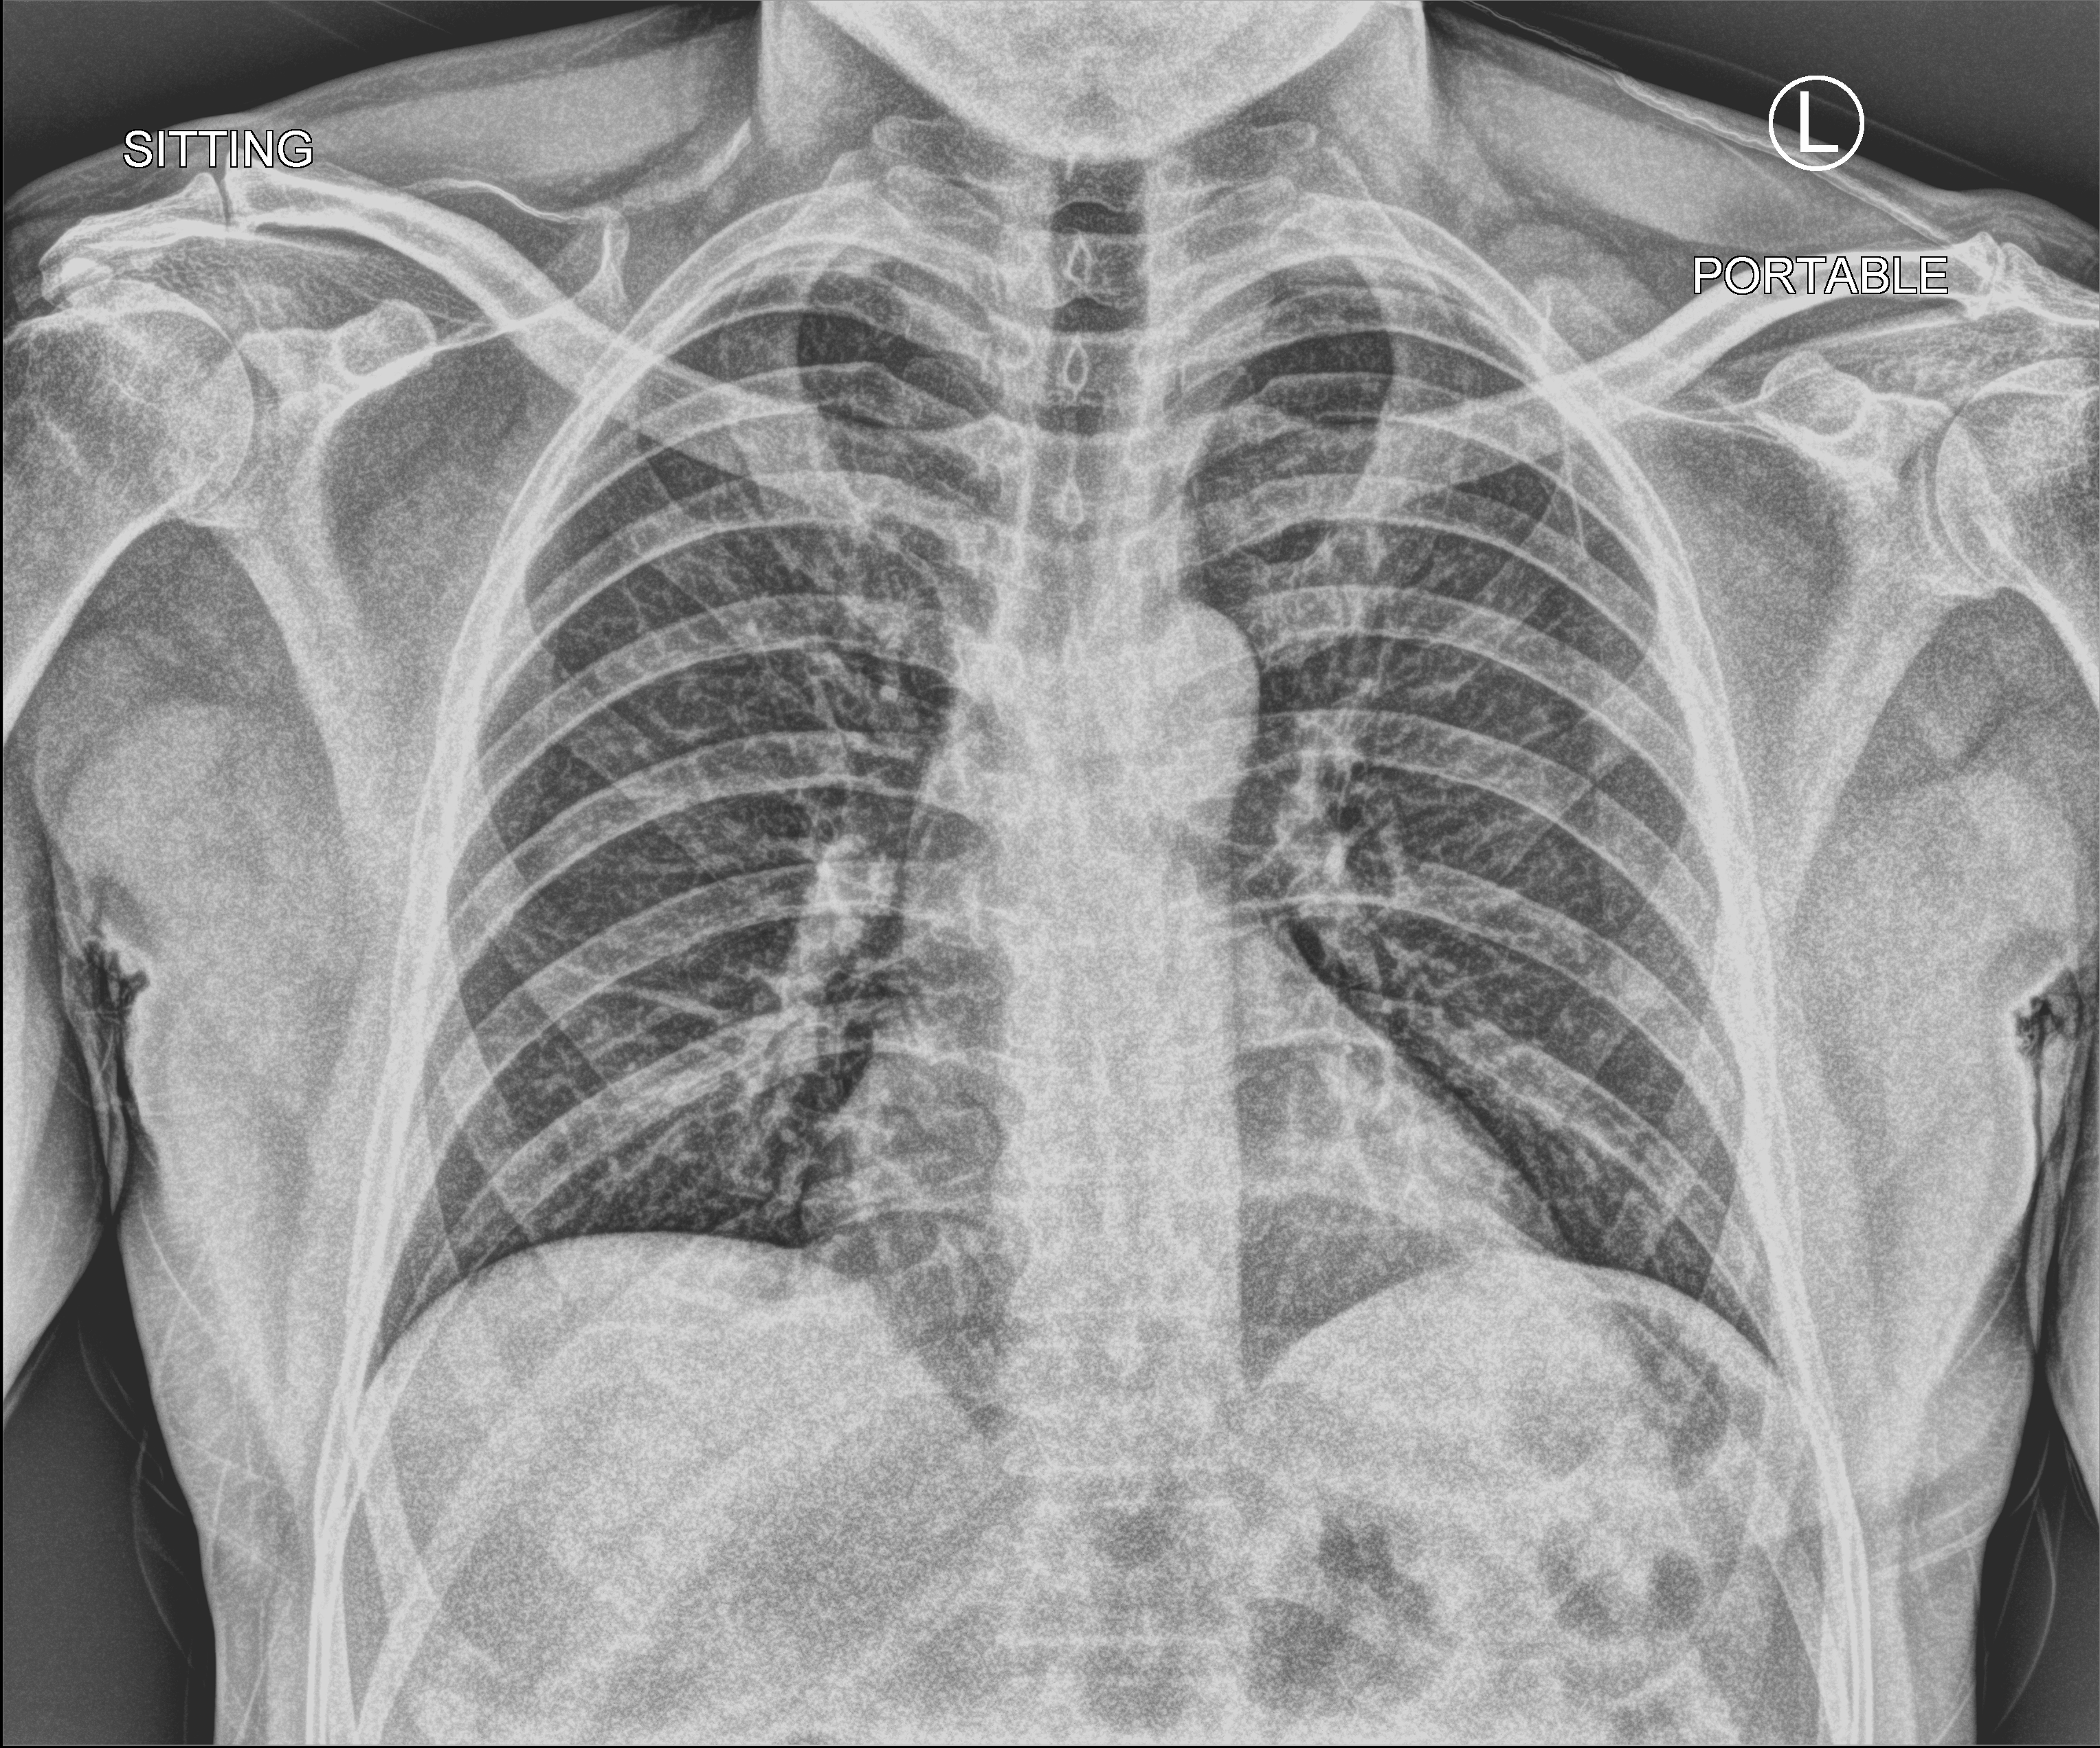
Portable chest radiograph; anteroposterior (AP) projection. Patient hospitalised with COVID-19; male, aged 18–59 years.
Hospital-stay facts (about this admission, not read from this image; timing relative to this image not recorded):
- other chronic lung disease (admission record): no
- length of hospital stay: 1 day